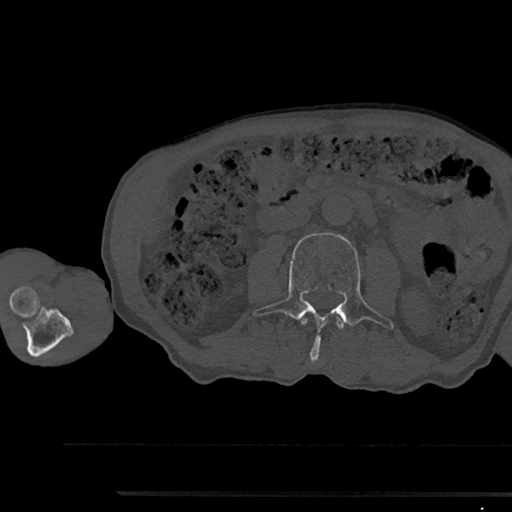
CT including the spine, one axial slice. Slice 500 of 797 in the series (ordered by position). 120 kVp. Bone window (W 1800 / L 400 HU). 512 × 512 image matrix. Patient: male, 79 years. Case-level facts recorded for this patient, not image findings: primary cancer: prostate.
Structures marked on this image (semi-automatically segmented with operator editing):
- L2 vertebra: box from (x=301, y=318) to (x=344, y=329) px
- L3 vertebra: (x=253, y=233)–(x=393, y=361)